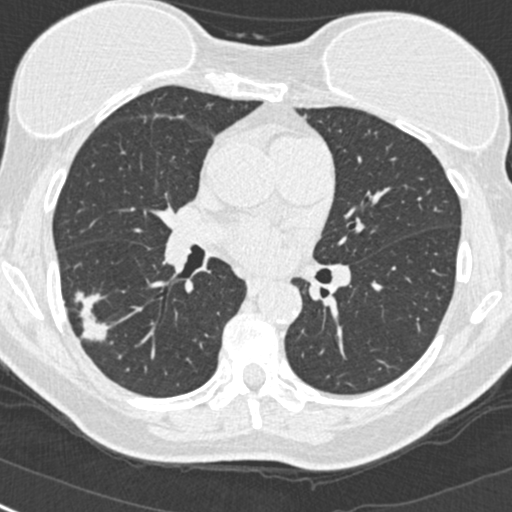
Low-dose screening chest CT, one axial slice. Slice 141 of 268 in the series (ordered by position). 120 kVp. Lung window (W 1500 / L -600 HU). 512 × 512 image matrix, field of view 296 × 296 mm.
Annotated regions visible in this slice (manually delineated by an expert):
- lesion 1 (tumor, upper lobe of right lung): bounding box (x1, y1, x2, y2) in pixels: (75, 292, 109, 341)